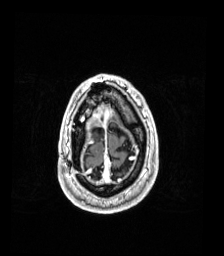
Brain MRI from a brain-tumour surgery series, one axial slice; position 26 of 192 along the scan axis; T1-weighted post-contrast; 1 mm slice thickness; 224 × 256 image matrix. From the clinical record (not read from this slice): histopathology: Astrocytoma; WHO grade: 4; IDH mutation: yes.
Outlined on this slice (manually delineated by an expert):
- previous resection cavity: bounding box <94,128,103,134> (left, top, right, bottom; pixels)